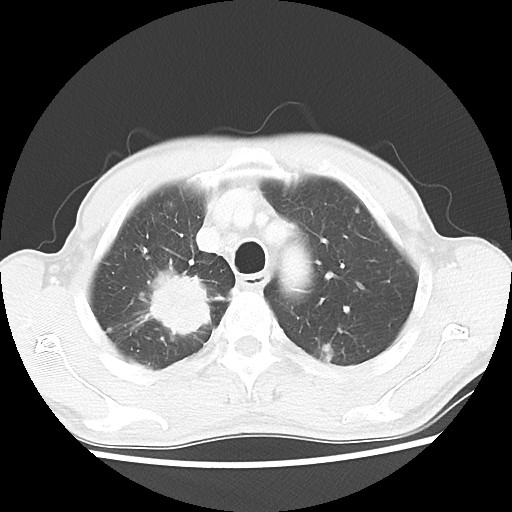
Chest CT, one axial slice. Position 42 of 52 along the scan axis. Reconstruction kernel LUNG. 100 kVp. Lung window (W 1500 / L -600 HU). 512 × 512 image matrix, field of view 323 × 323 mm. Patient: male, 66 years. From the clinical record (not read from this slice): clinical TNM (as recorded): T2 N0 M1a.
Annotated regions visible in this slice (bounding box drawn by a radiologist):
- lung tumour (recorded histology: adenocarcinoma): box from (x=132, y=261) to (x=218, y=339) px